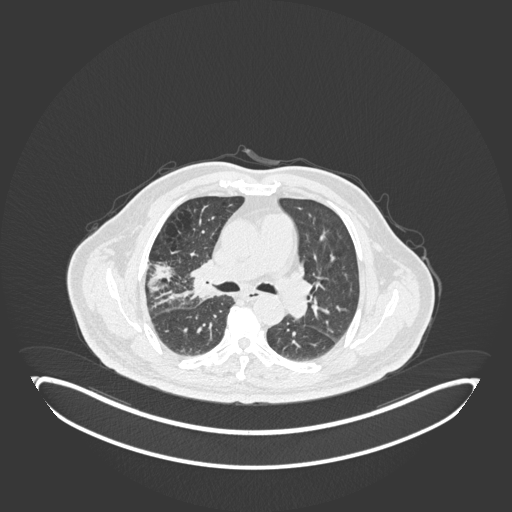
Chest CT, one axial slice; slice 104 of 247 in the series (ordered by position); 120 kVp; lung window (W 1500 / L -600 HU); 512 × 512 image matrix, field of view 500 × 500 mm. Patient: male, 72 years. From the clinical record (not read from this slice): clinical TNM (as recorded): T1c N0 M0.
Structures marked on this image (rectangle marked by the reading radiologist):
- lung tumour (recorded histology: squamous cell carcinoma): bounding box [x1, y1, x2, y2] px = [183, 253, 215, 311]